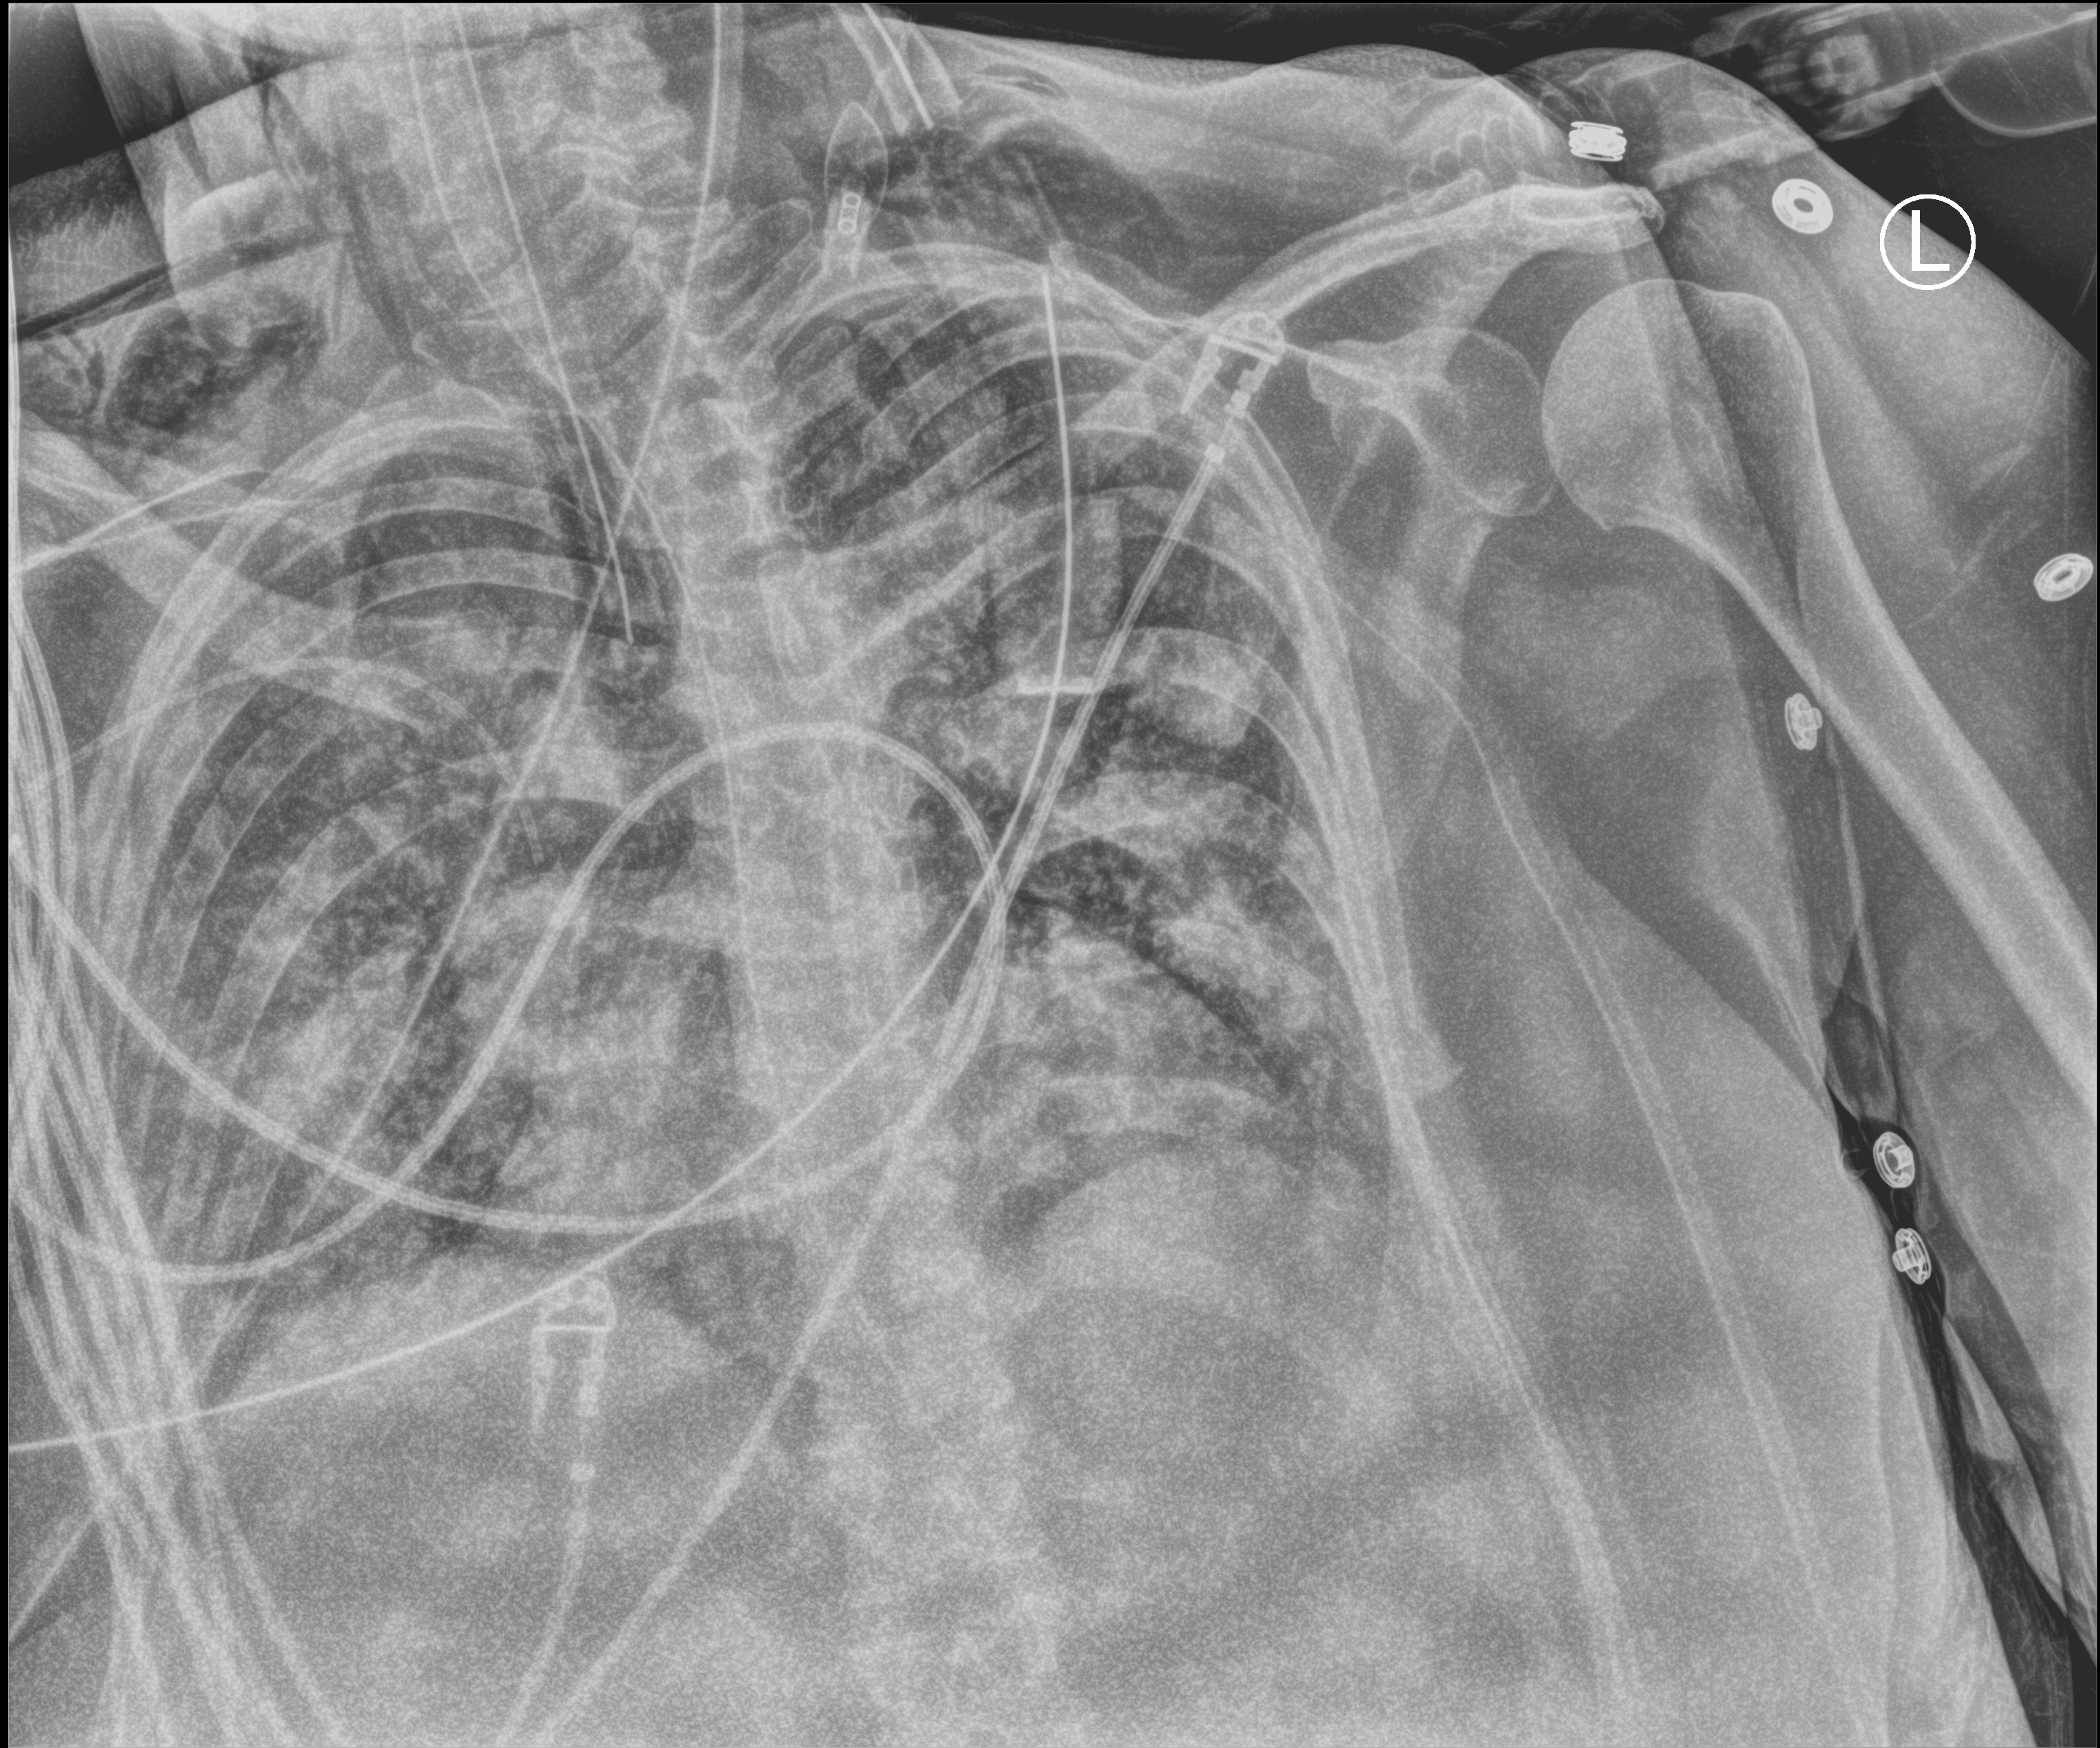
Chest X-ray (portable). Patient hospitalised with COVID-19; female, aged 60–74 years.
From the hospital-stay record, not from the radiograph (when in the stay this image was taken is not recorded): chronic kidney disease (admission record): no.